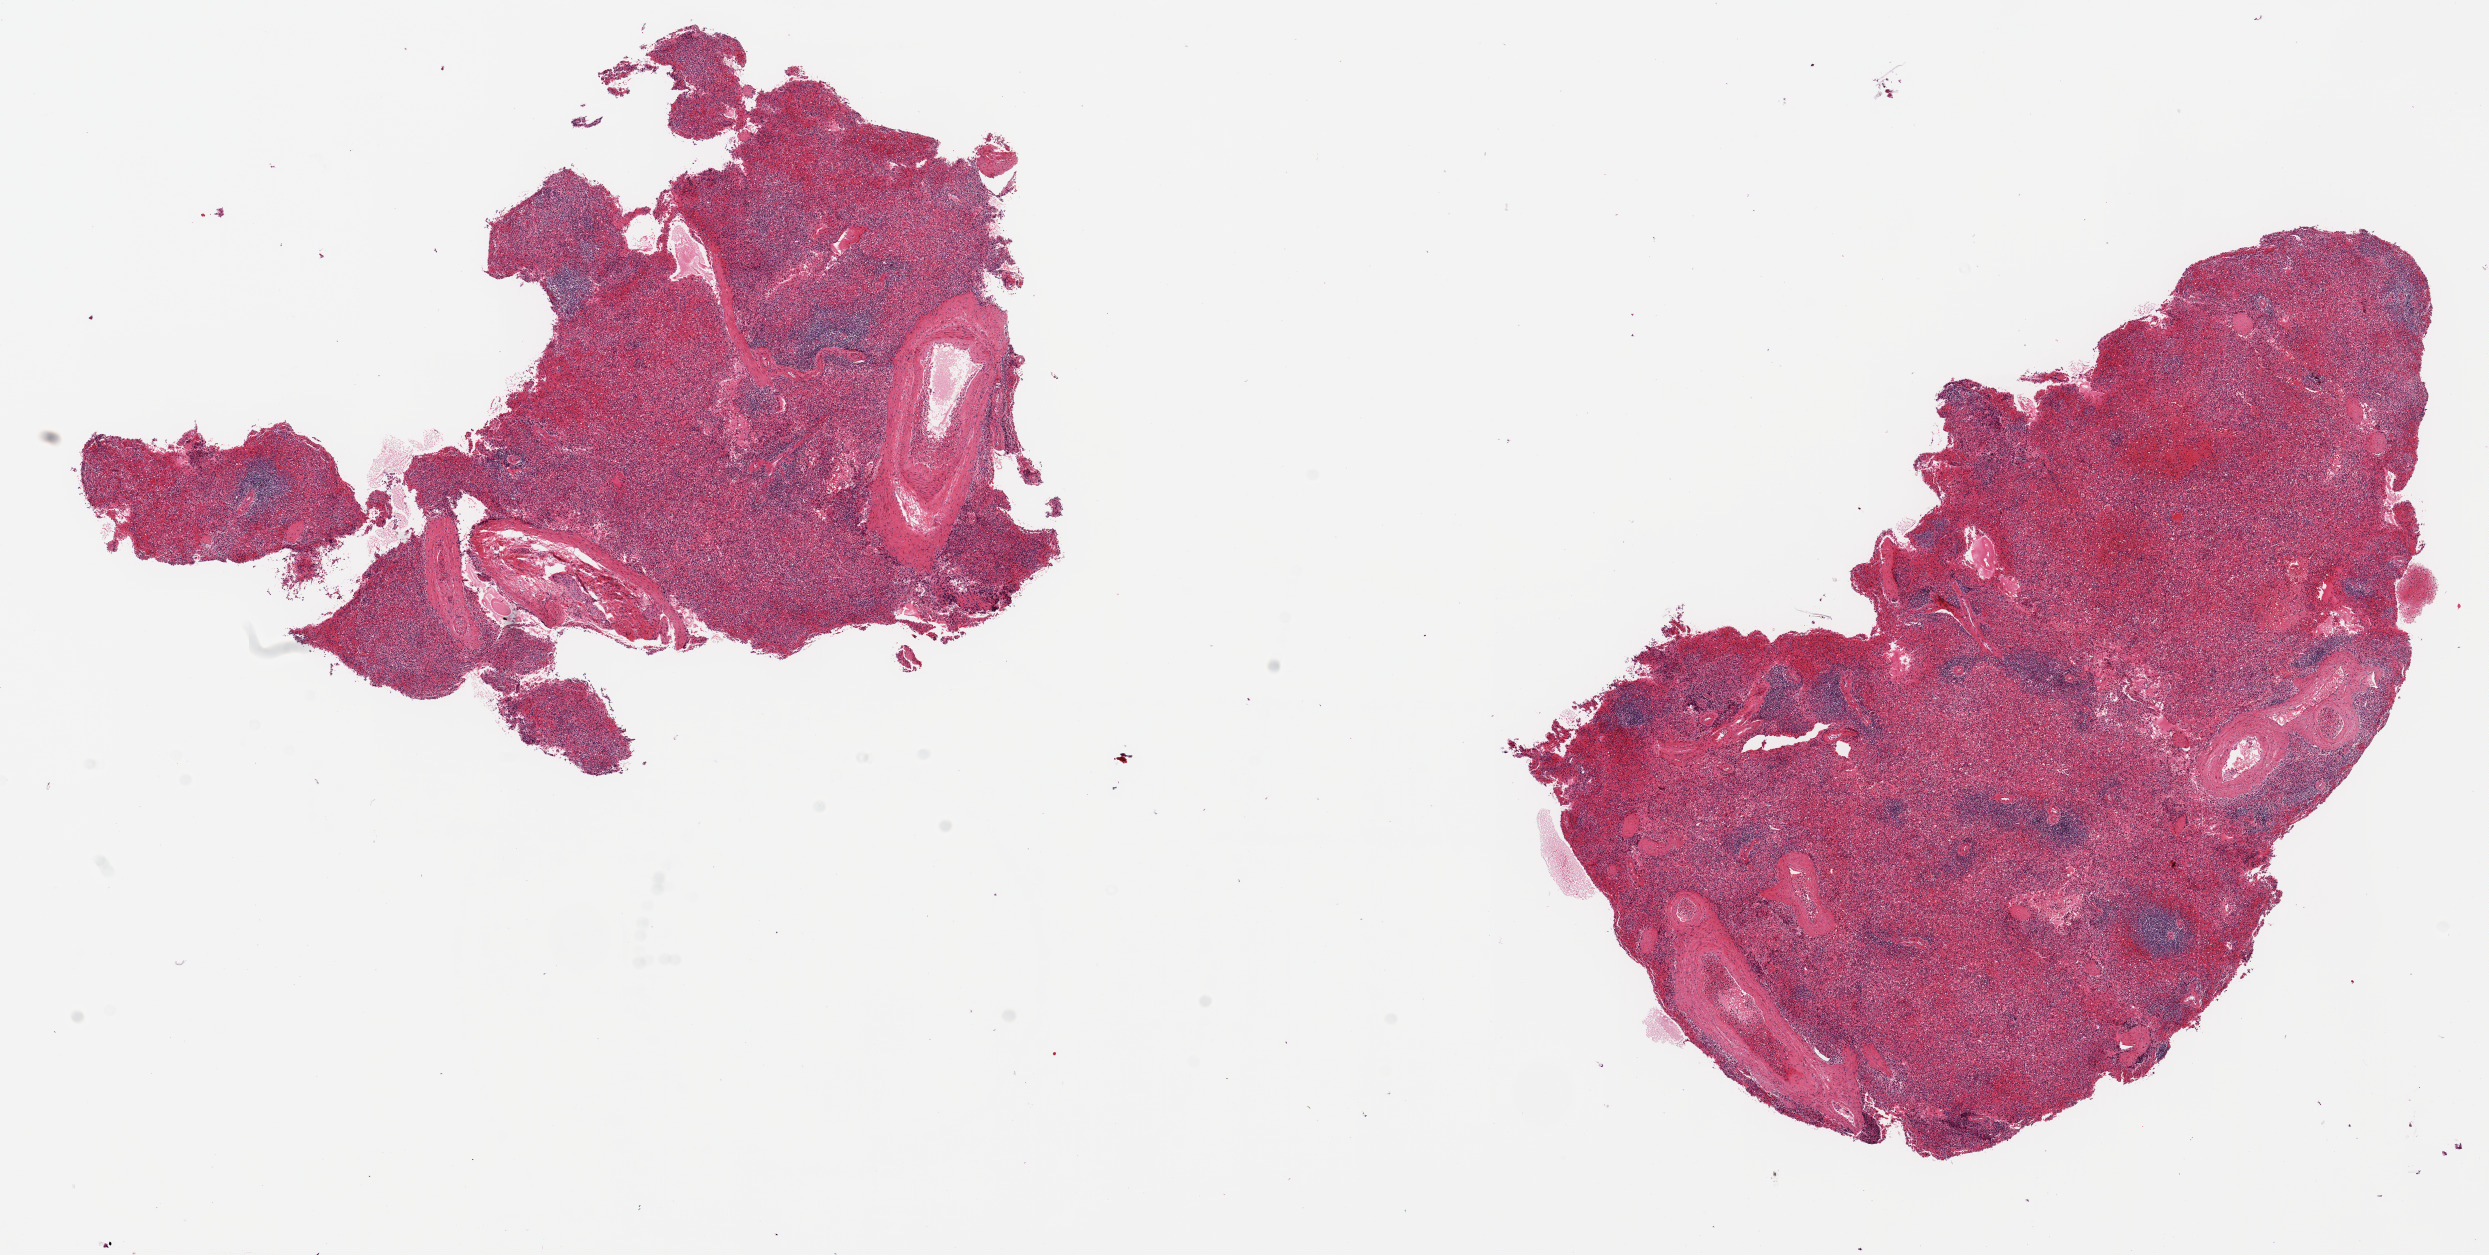
Digitized haematoxylin and eosin-stained section, brightfield — whole scanned area (about 19.7 x 9.9 mm, slide scanned at 20x) shown as a low-resolution overview. PAXgene-fixed paraffin-embedded (PFPE) section. Section of spleen (target tissue). Tissue donor sample. Female donor.
Review note (as recorded): 2 pieces; several large blood vessels.